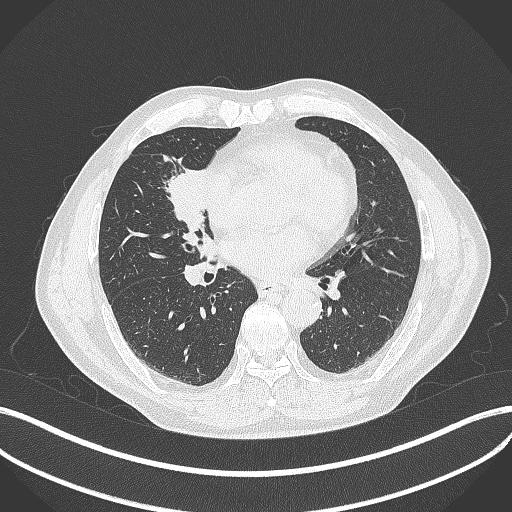
Chest CT, one axial slice. Slice 186 of 429 in the series (ordered by position). 120 kVp. Lung window (W 1500 / L -600 HU). 1 mm slice thickness. 512 × 512 image matrix. Patient: male, 61 years. From the clinical record (not read from this slice): clinical TNM (as recorded): T2b N1 M0.
Outlined on this slice (bounding box drawn by a radiologist):
- lung tumour (recorded histology: squamous cell carcinoma): bounding box [x1, y1, x2, y2] px = [155, 156, 208, 236]